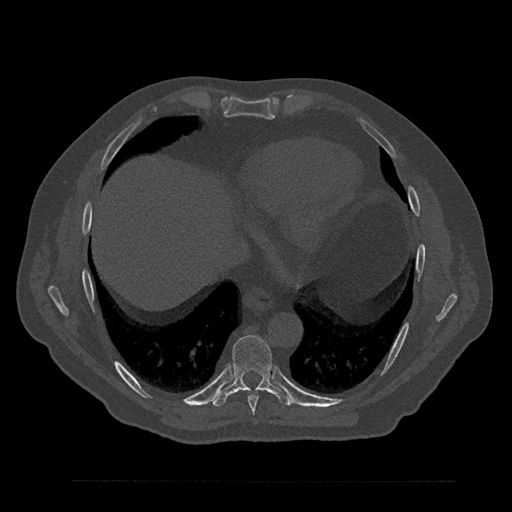
CT including the spine, one axial slice. Position 424 of 797 along the scan axis. Bone window (W 1800 / L 400 HU). 0.5 mm slice thickness. 512 × 512 image matrix, field of view 430 × 430 mm. Patient: male, 61 years. From the clinical record (not read from this slice): primary cancer: prostate.
Outlined on this slice (semi-automatically segmented with operator editing):
- T8 vertebra: bounding box (x1, y1, x2, y2) in pixels: (240, 390, 259, 414)
- T9 vertebra: (213, 335, 292, 407)